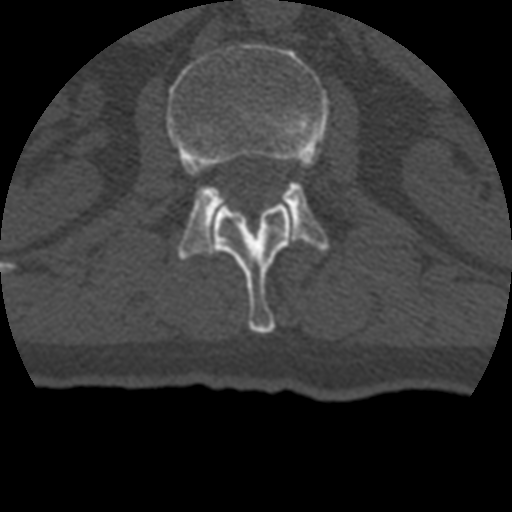
CT including the spine, one axial slice; slice 131 of 399 in the series (ordered by position); reconstruction kernel STANDARD; 120 kVp; bone window (W 1800 / L 400 HU); 512 × 512 image matrix, field of view 160 × 160 mm. Patient age 69 years. From the clinical record (not read from this slice): primary cancer: prostate.
Outlined on this slice (semi-automatic segmentation, software-assisted and operator-edited):
- L1 vertebra: bounding box <211,199,294,334> (left, top, right, bottom; pixels)
- L2 vertebra: <166,44,329,259>